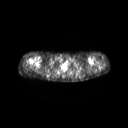
FDG PET of an extremity soft-tissue mass (from a PET/CT study), one axial slice. Slice 216 of 267 in the series (ordered by position). 3.27 mm slice thickness. 128 × 128 image matrix, field of view 600 × 600 mm. Female patient, age 28 years. From the clinical record (not read from this slice): histological type: malignant fibrous histiocytoma; grade: low; site of the primary tumour: left arm.
Outlined on this slice (expert contour drawn on MRI and transferred to this co-registered scan by the dataset authors):
- gross tumour volume (mass): bounding box [x1, y1, x2, y2] px = [99, 67, 101, 69]